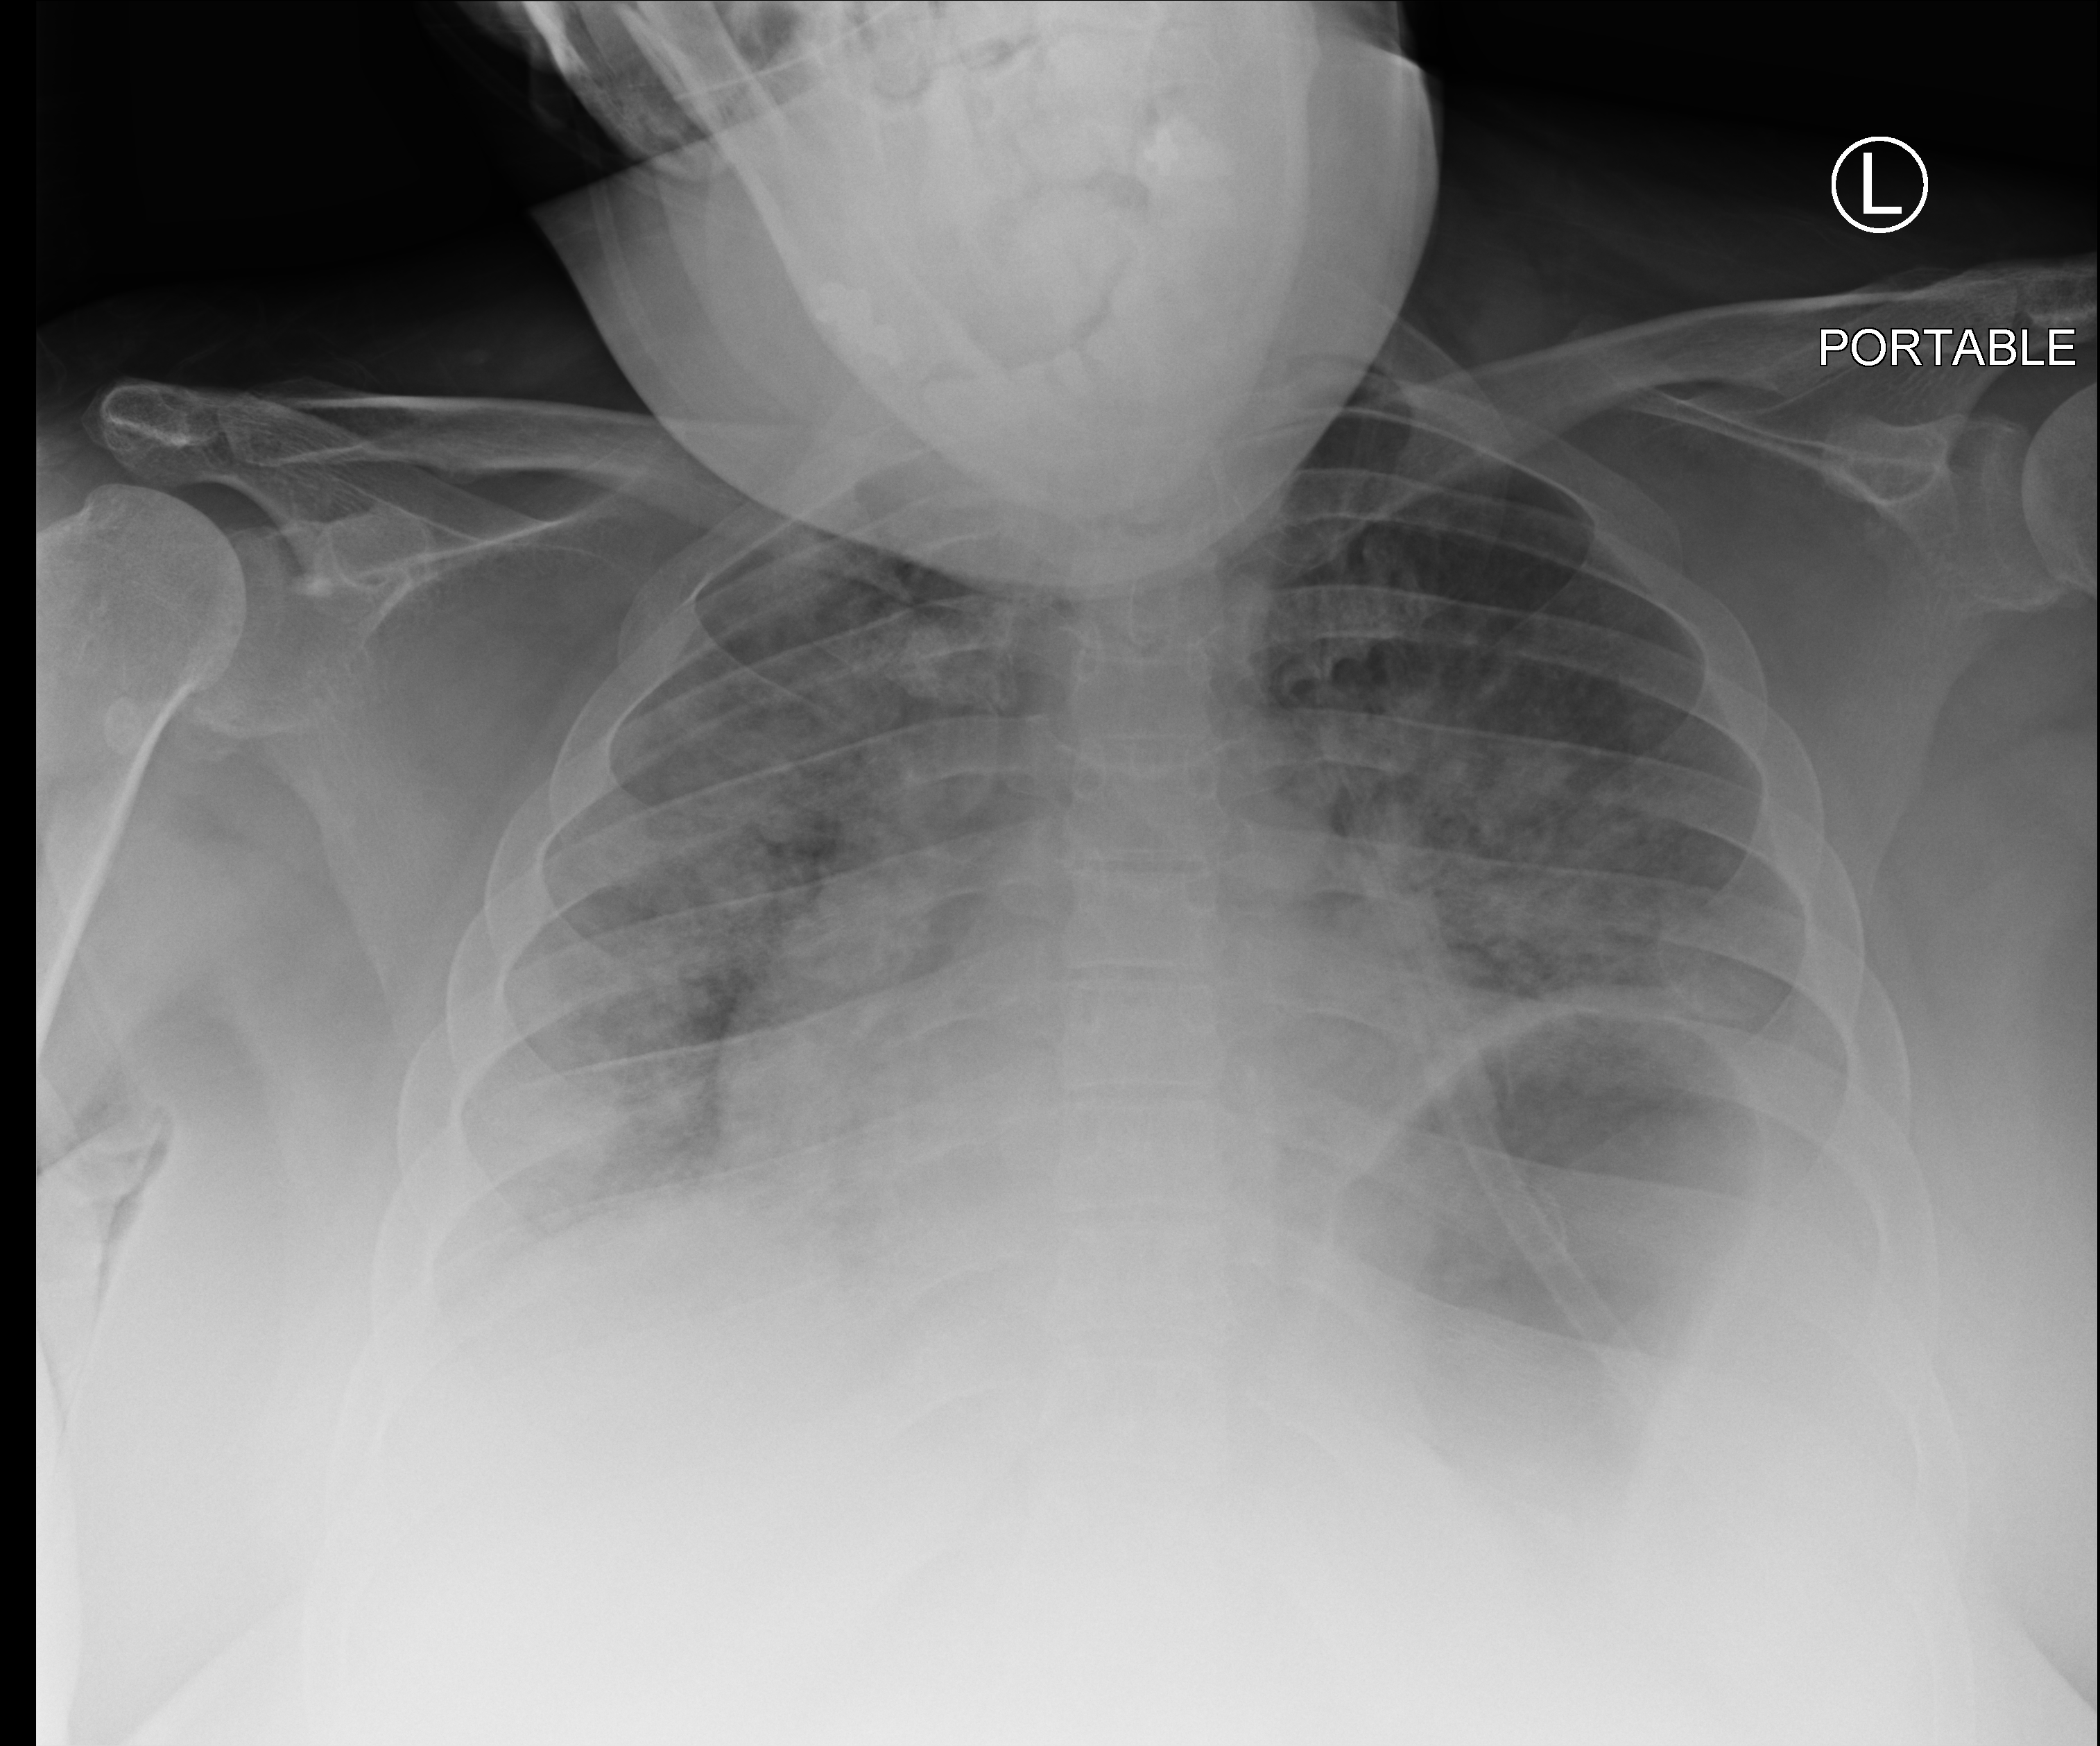
Portable chest radiograph; anteroposterior (AP) projection. Female patient hospitalised with COVID-19, age 18–59 years.
Admission-level facts for this patient (not findings on this image; timing relative to this image not recorded): admitted to intensive care during this hospital stay: no; length of hospital stay: 6 days.